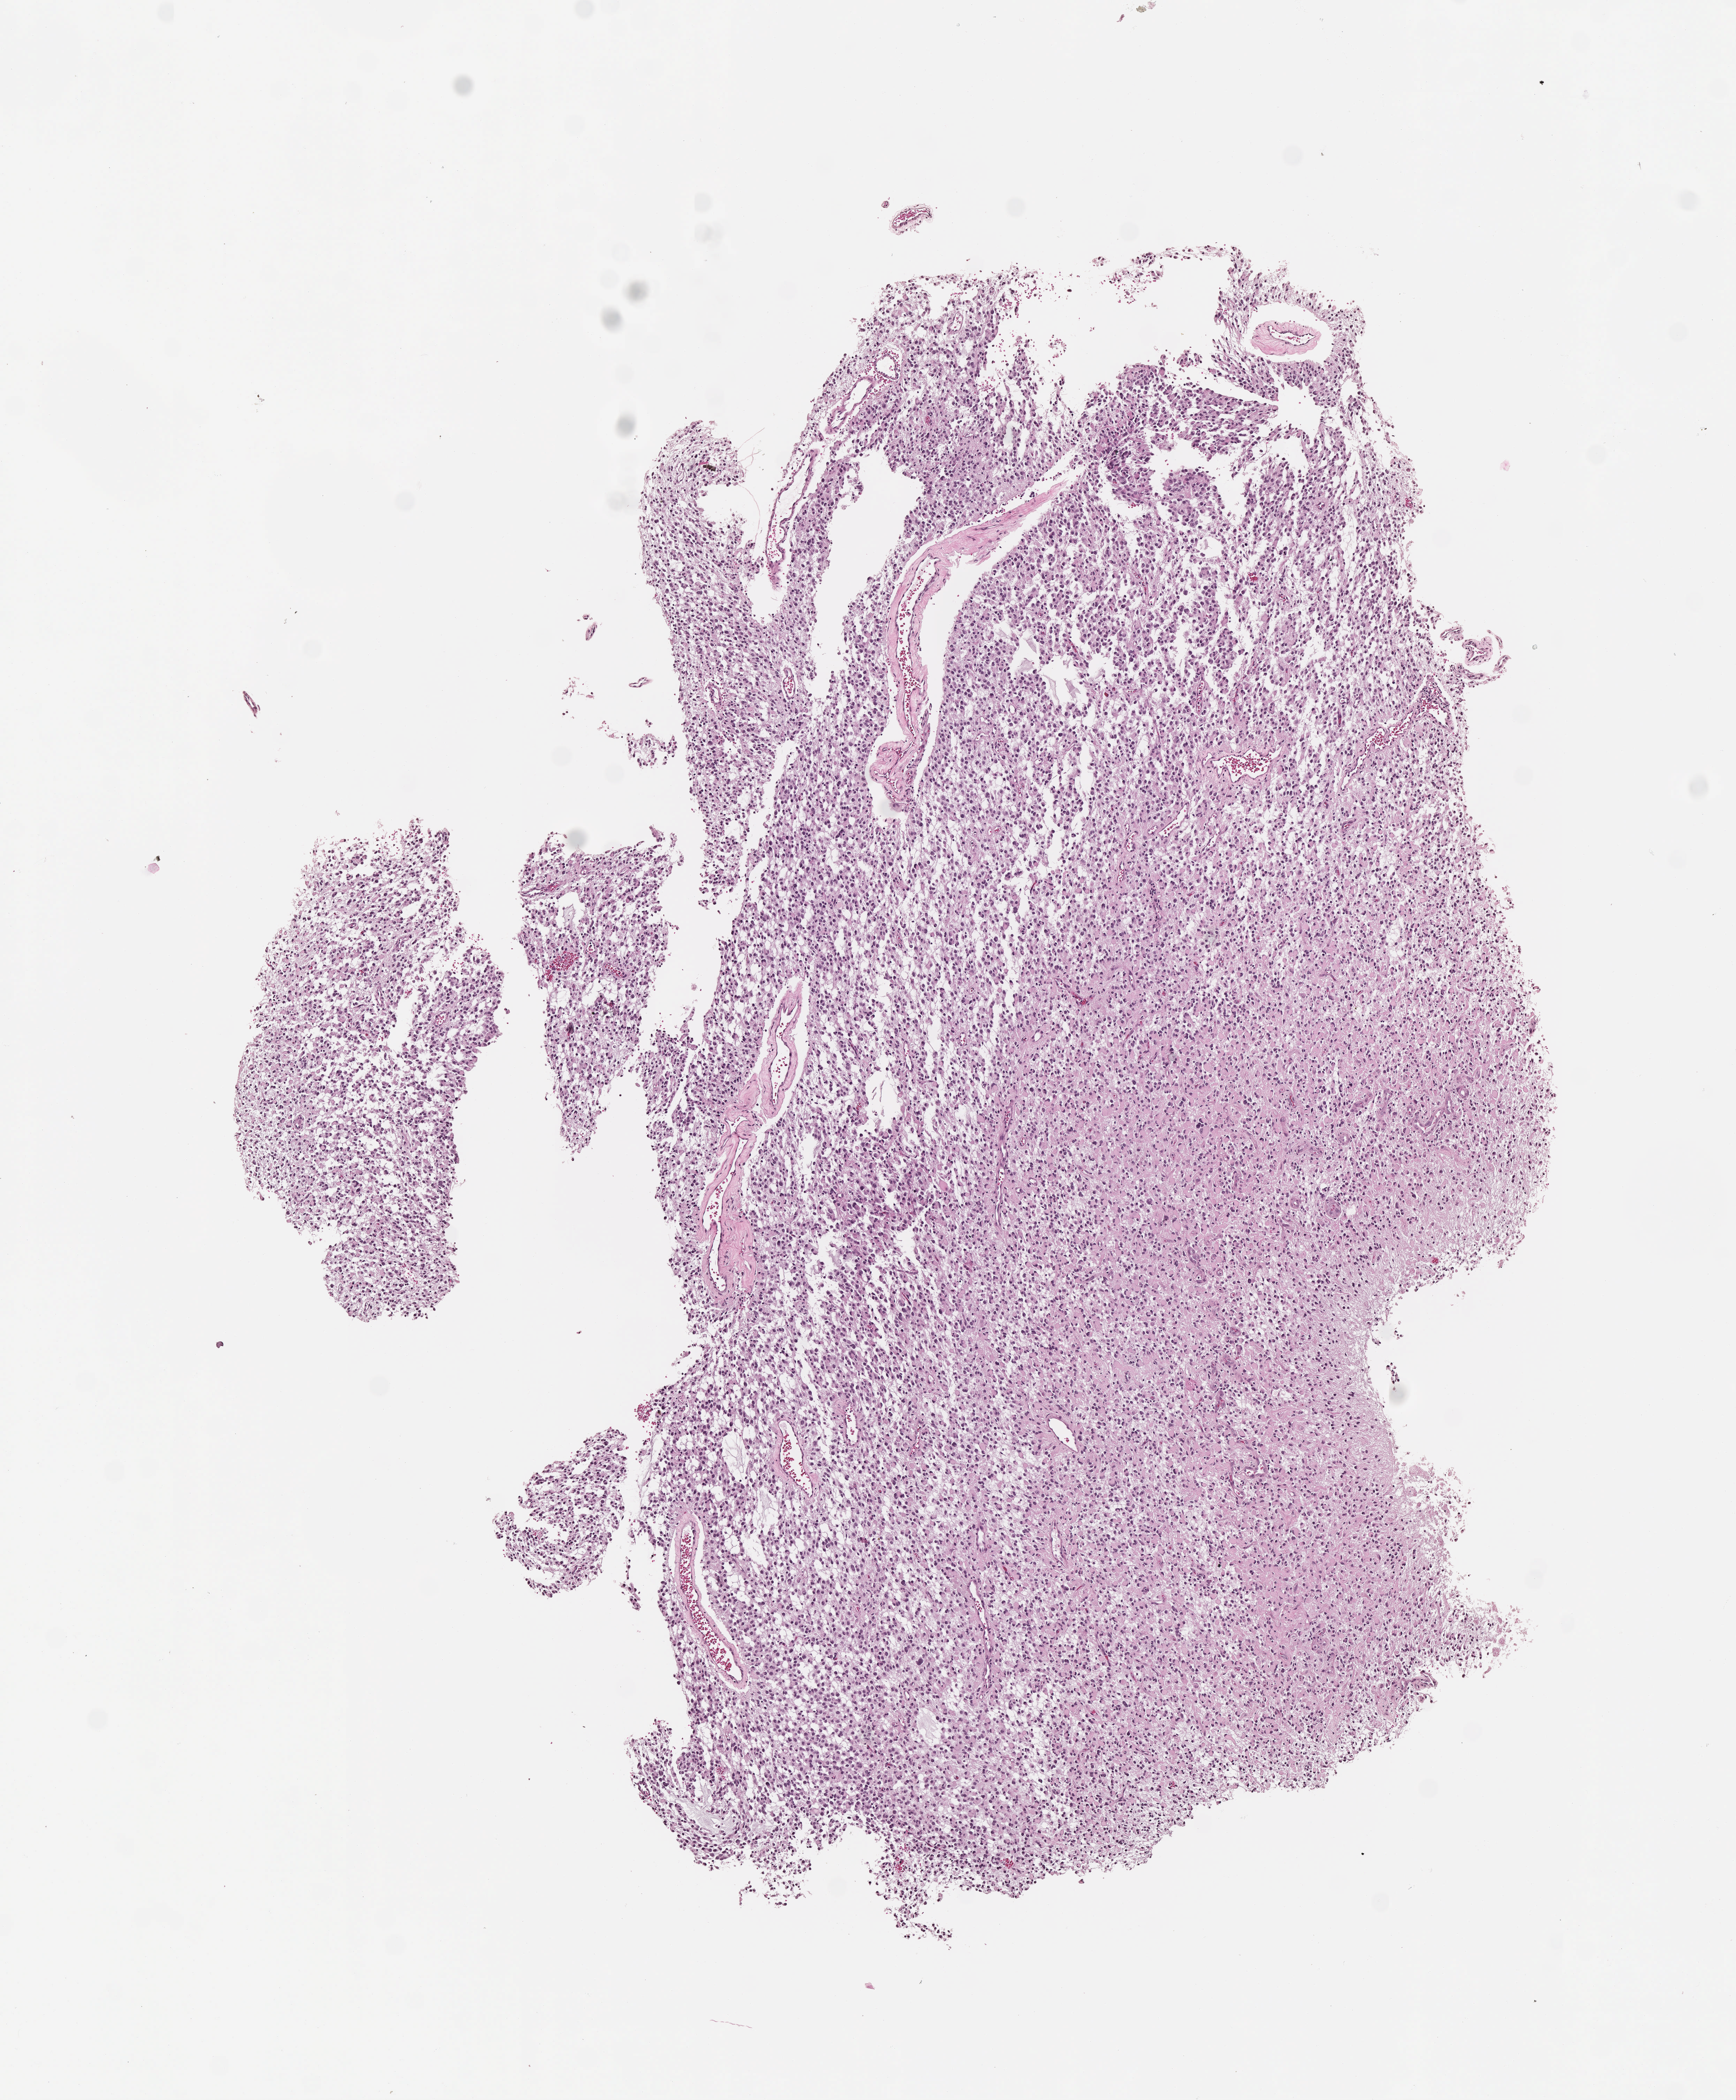
Whole-slide histology image, H&E, low-resolution overview of the scanned area, about 5.0 x 6.1 mm (from a 40x scan); FFPE section; primary tumour sample from the brain. Patient: male, age at initial diagnosis 32 years. Histologic grade: G2 (moderately differentiated).
* diagnosis: Oligodendroglioma, NOS (cerebrum)
* laterality: right